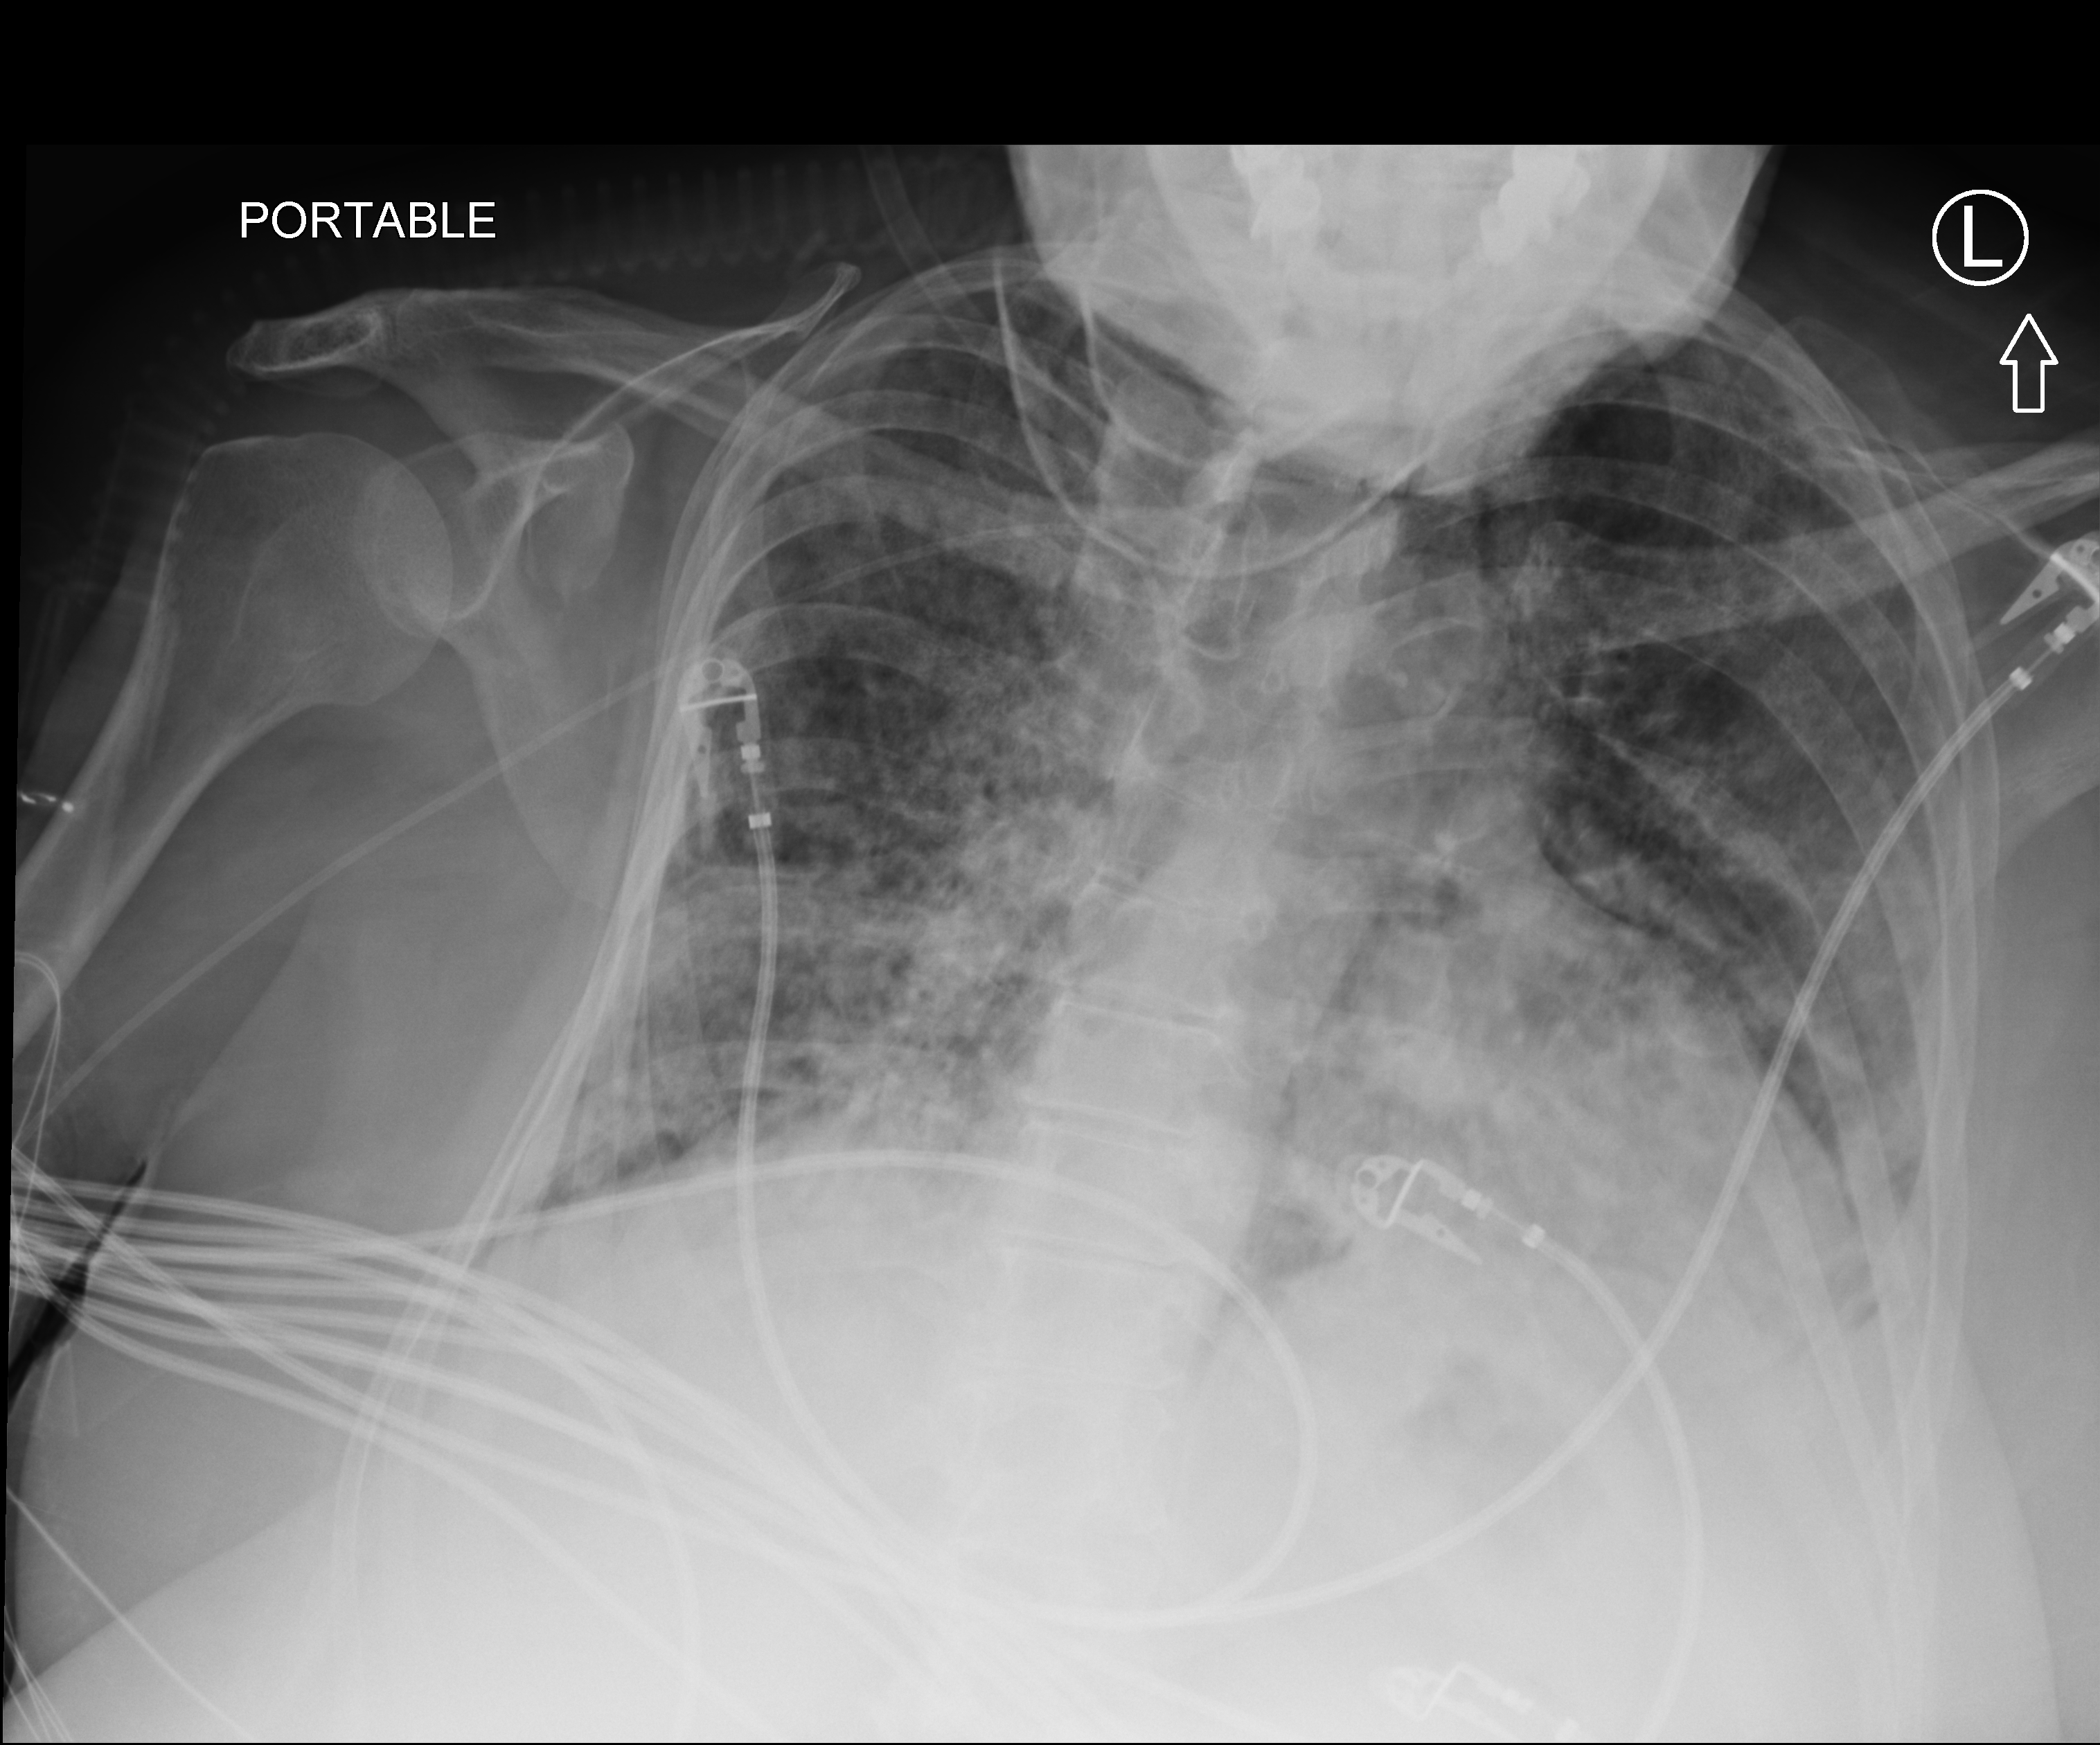
Chest X-ray (portable), anteroposterior (AP) projection. Patient hospitalised with COVID-19; female, aged 60–74 years.
Admission-level facts for this patient (not findings on this image; timing relative to this image not recorded):
- smoking status (admission record): never
- admitted to intensive care during this hospital stay: yes
- mechanically ventilated during this hospital stay: yes